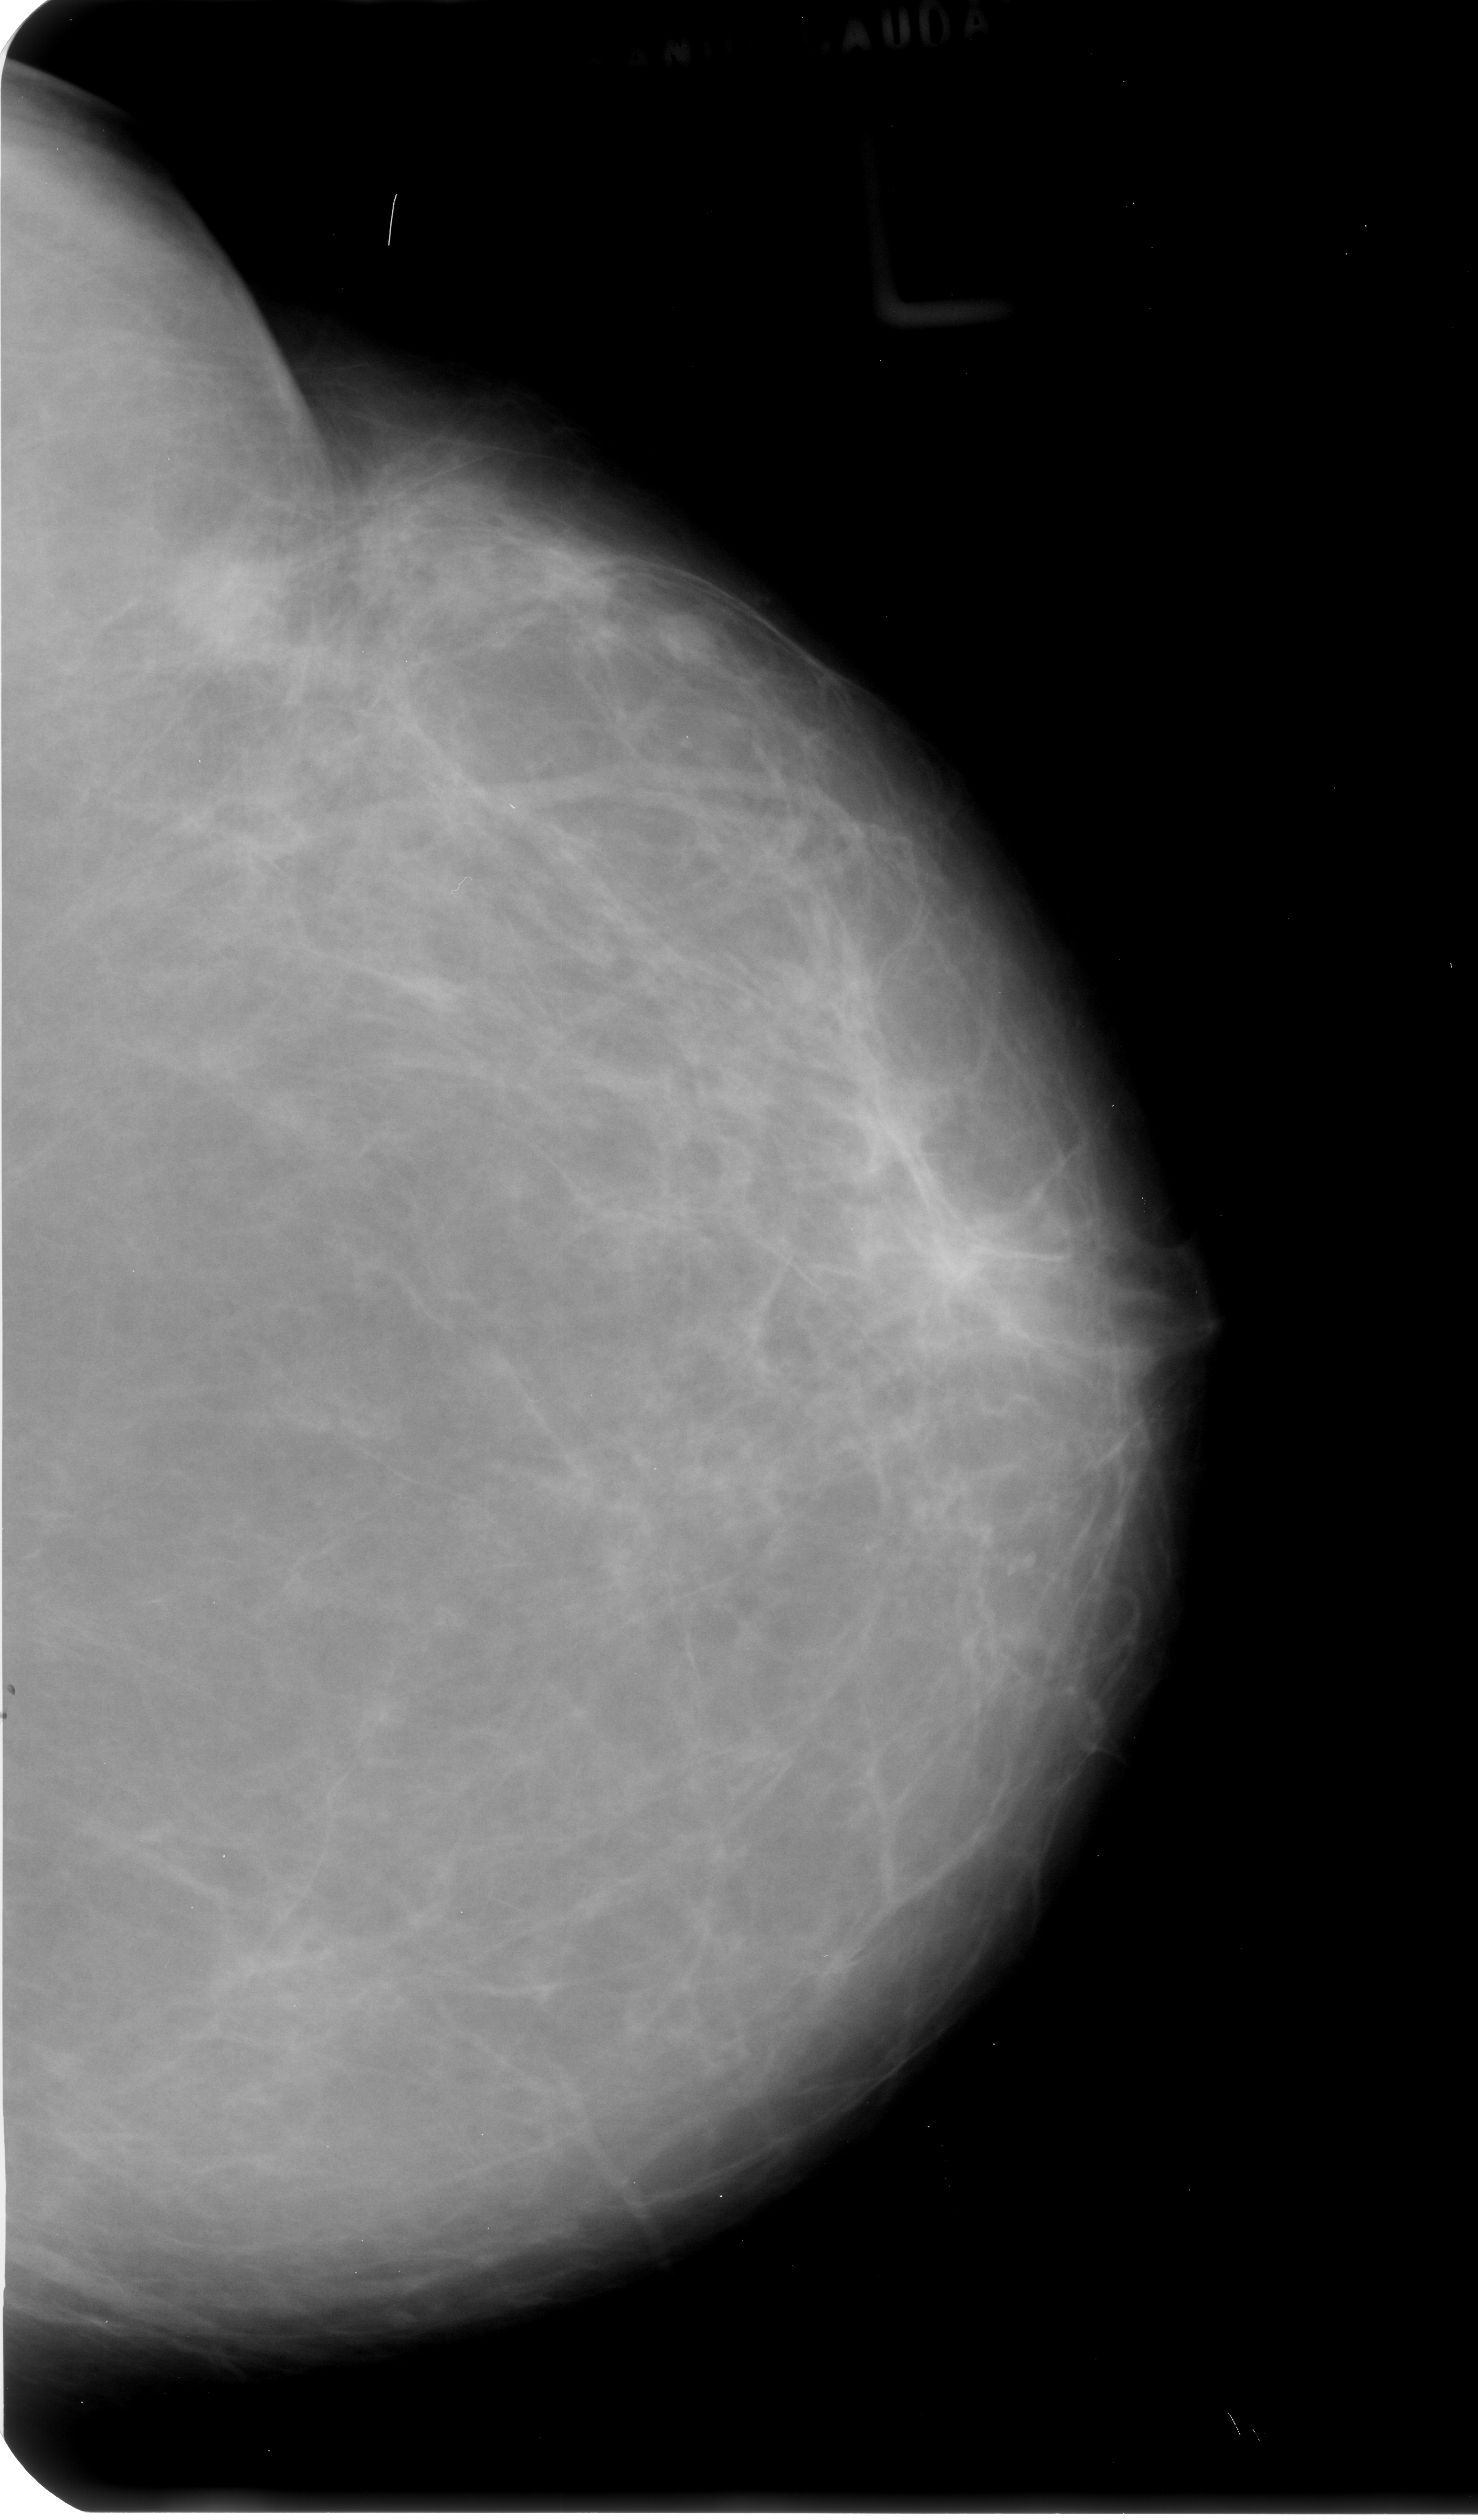
Scanned film-screen mammogram. Left breast. Craniocaudal (CC) view. BI-RADS breast density category 2 (scale 1–4). 1478 × 2520 image matrix.
Marked abnormalities (boxes around the expert regions of interest):
- mass, shape irregular, margins spiculated; BI-RADS assessment category 4; pathology result (as recorded, not read from the image): malignant: bounding box [x1, y1, x2, y2] px = [175, 539, 289, 680]